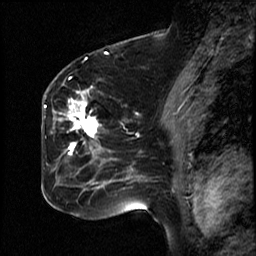
Breast MRI (dynamic contrast-enhanced), one sagittal slice; slice 29 of 50 in the series (ordered by position); dynamic contrast-enhanced study with each time point stored as its own series, time point 2 of 4 at this slice position (early post-contrast, ordered by acquisition time); 1.5 T; TE 4.2 ms, TR 18.5 ms; 3 mm slice thickness; 256 × 256 image matrix, field of view 200 × 200 mm. Female patient, age 44 years. Case-level facts recorded for this patient, not image findings: setting: breast cancer imaged before/during neoadjuvant chemotherapy; receptor status: HR-positive, HER2-negative.
Outlined on this slice (semi-automatic segmentation, software-assisted and operator-edited):
- analysis volume of interest (the breast-tissue region the enhancement analysis was run in; not a lesion): bounding box <59,80,114,203> (left, top, right, bottom; pixels)
- tumour enhancement mask (voxels above the 100 % enhancement threshold inside the analysis volume of interest): <64,92,100,151>